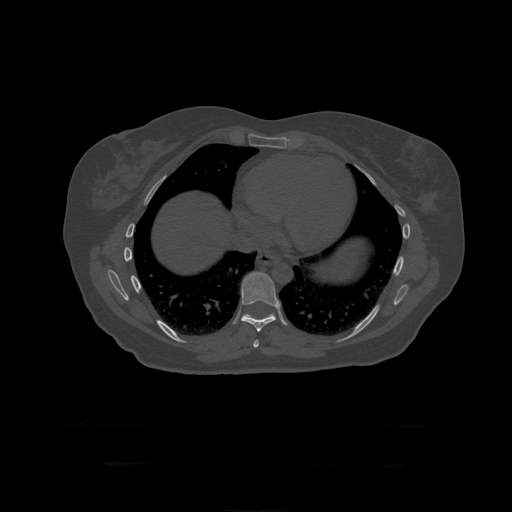
CT including the spine, one axial slice; position 258 of 399 along the scan axis; 120 kVp; bone window (W 1800 / L 400 HU); 1.25 mm slice thickness; 512 × 512 image matrix, field of view 450 × 450 mm. Patient age 41 years. From the clinical record (not read from this slice): primary cancer: breast.
Outlined on this slice (semi-automatic segmentation, software-assisted and operator-edited):
- T10 vertebra: bounding box [x1, y1, x2, y2] px = [244, 314, 274, 319]
- T8 vertebra: [253, 340, 259, 348]
- T9 vertebra: [241, 272, 281, 332]